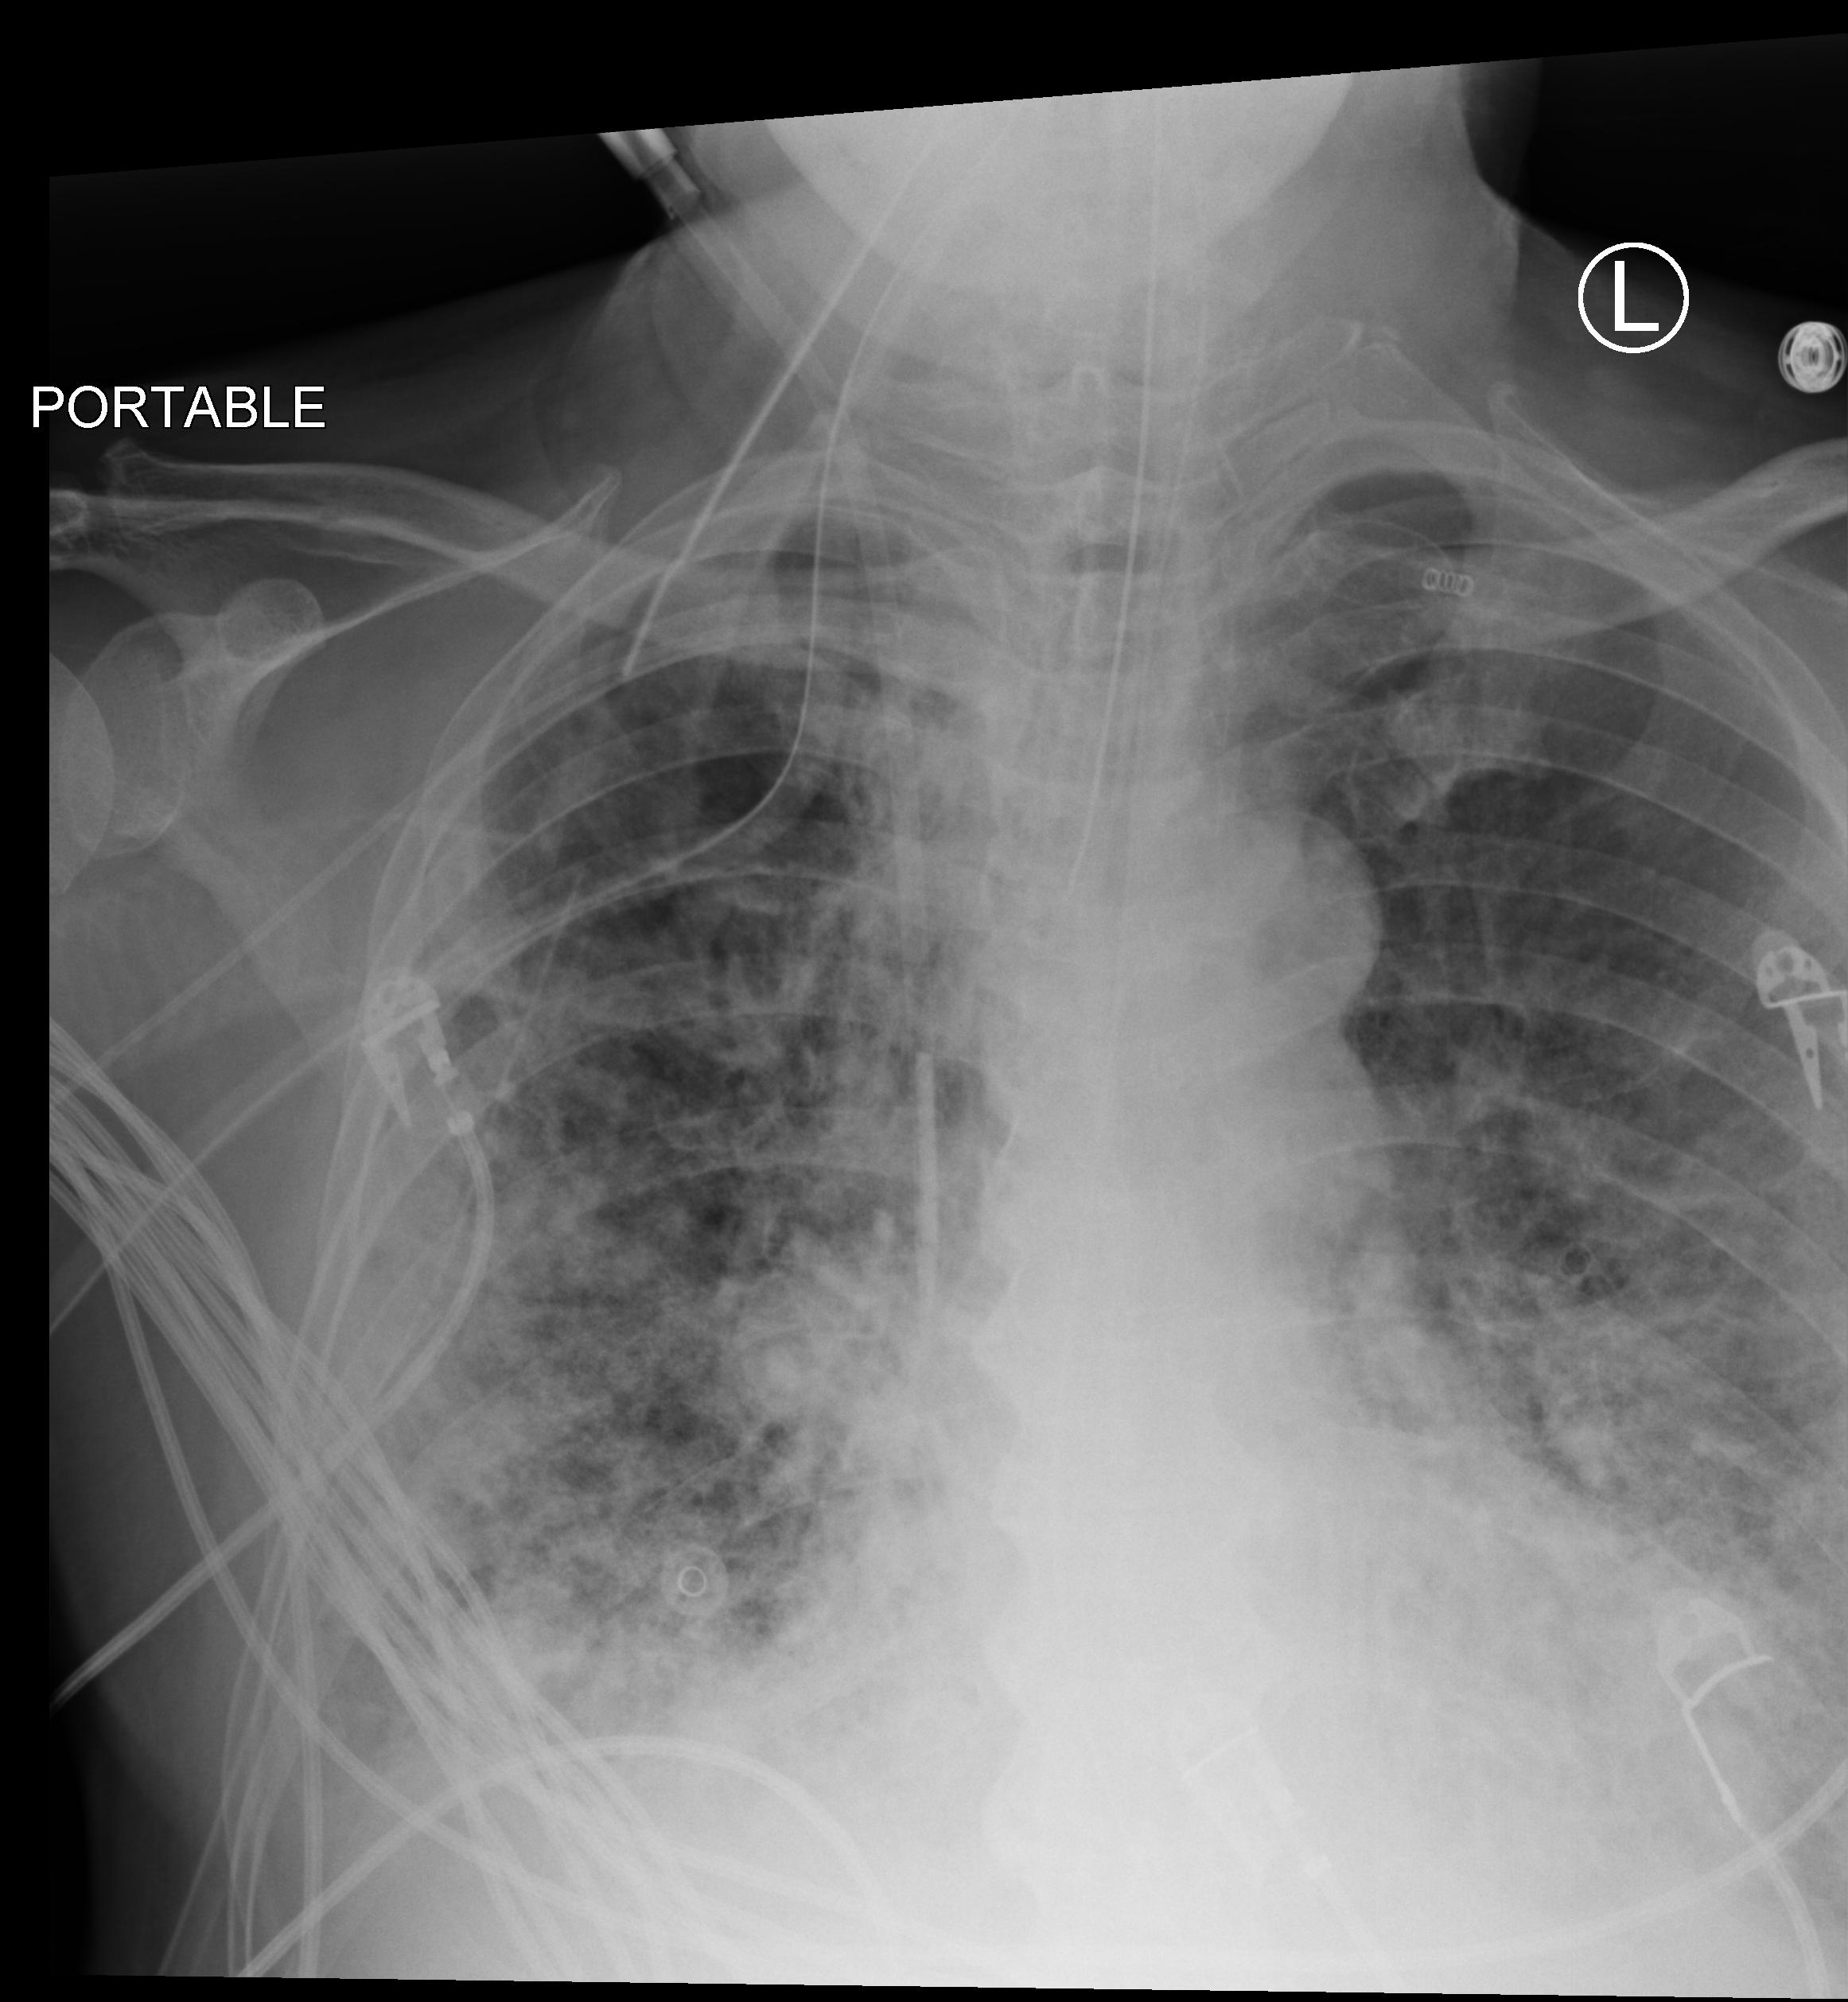
Chest X-ray (portable), anteroposterior (AP) projection. Male patient hospitalised with COVID-19, age 60–74 years.
Hospital-stay facts (about this admission, not read from this image; timing relative to this image not recorded):
- admitted to intensive care during this hospital stay: yes